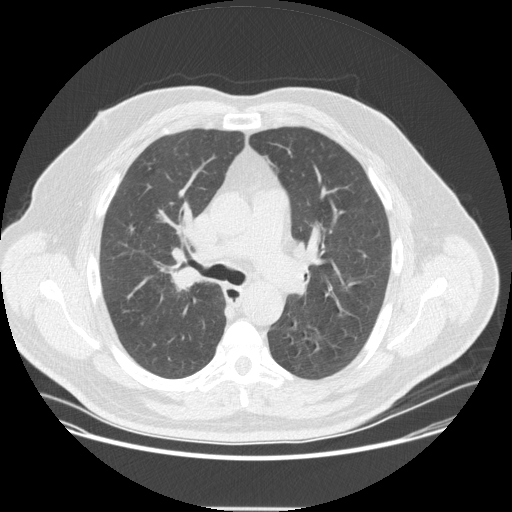
Low-dose screening chest CT, axial slice. Second annual screen. Lung window (W 1500 / L -600 HU). 120 kVp. Slice 126 of 351 in the series. Male participant, aged 57 years at enrolment. Current smoker at enrolment.
Lesion marked by an expert reader, bounding box (x1, y1, x2, y2) in pixels: (154, 254, 211, 306). Reader record for this screening exam (exam-level; its link to the box is not recorded): non-calcified nodule or mass ≥4 mm, right upper lobe, 20 × 16 mm, spiculated (stellate) margins, soft tissue attenuation, pre-existing on the prior screen: no. Official screen result: positive, other. Participant outcome: lung cancer diagnosed 35 days after this screen — non-small cell carcinoma, right upper lobe, poorly differentiated (G3), stage IIA (AJCC 6th edition), 25 mm at pathology.